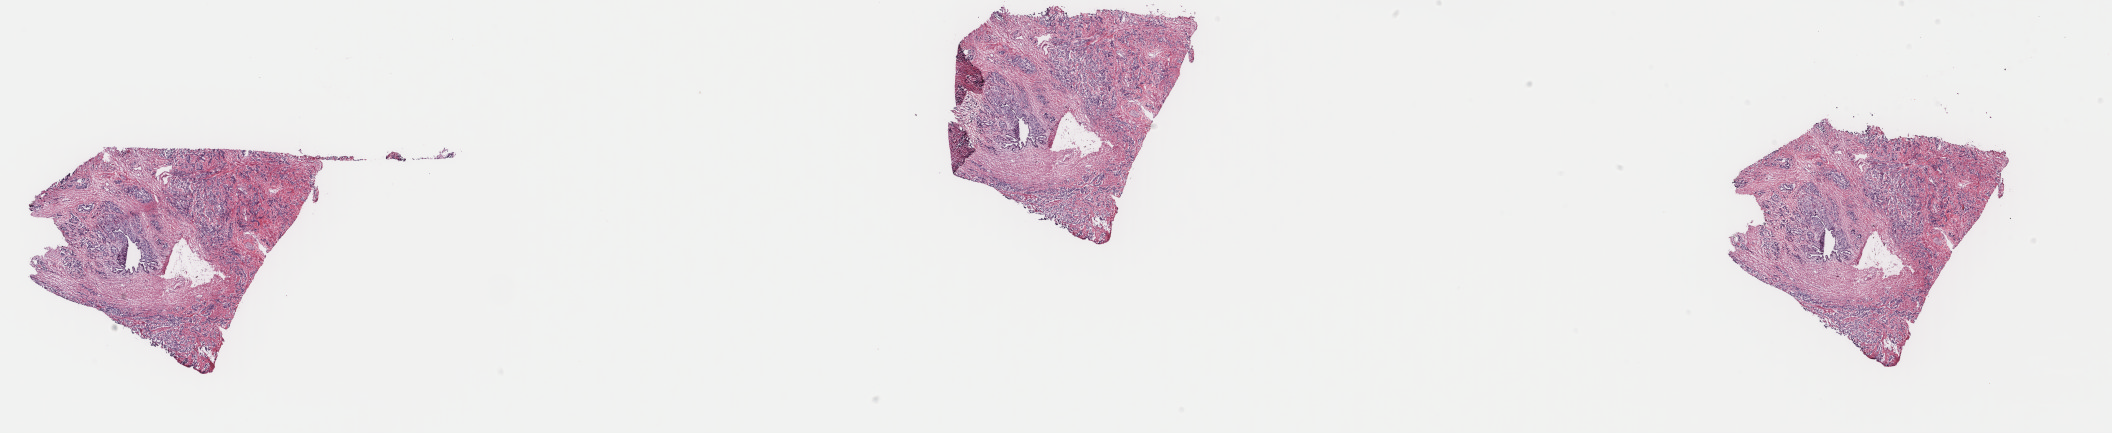
Digitized Hematoxylin and eosin (H&E) stained tissue section (whole slide), low-resolution overview of the scanned area, about 33.5 x 6.9 mm (slide scanned at 40x); frozen section; prostate, primary tumour sample. Male patient; age at initial diagnosis 73 years. Gleason score: 7 (3+4). Pathologist review of this section (percent, as recorded): tumour cells 50%, tumour nuclei 70%, normal cells 40%, stromal cells 10%, necrosis 0%. Inflammatory infiltration, as recorded: lymphocyte infiltration 0%, monocyte infiltration 0%, neutrophil infiltration 0%.
Lymph nodes positive (case pathology): 0 of 4 examined. Histologic diagnosis: Adenocarcinoma, NOS (prostate gland).